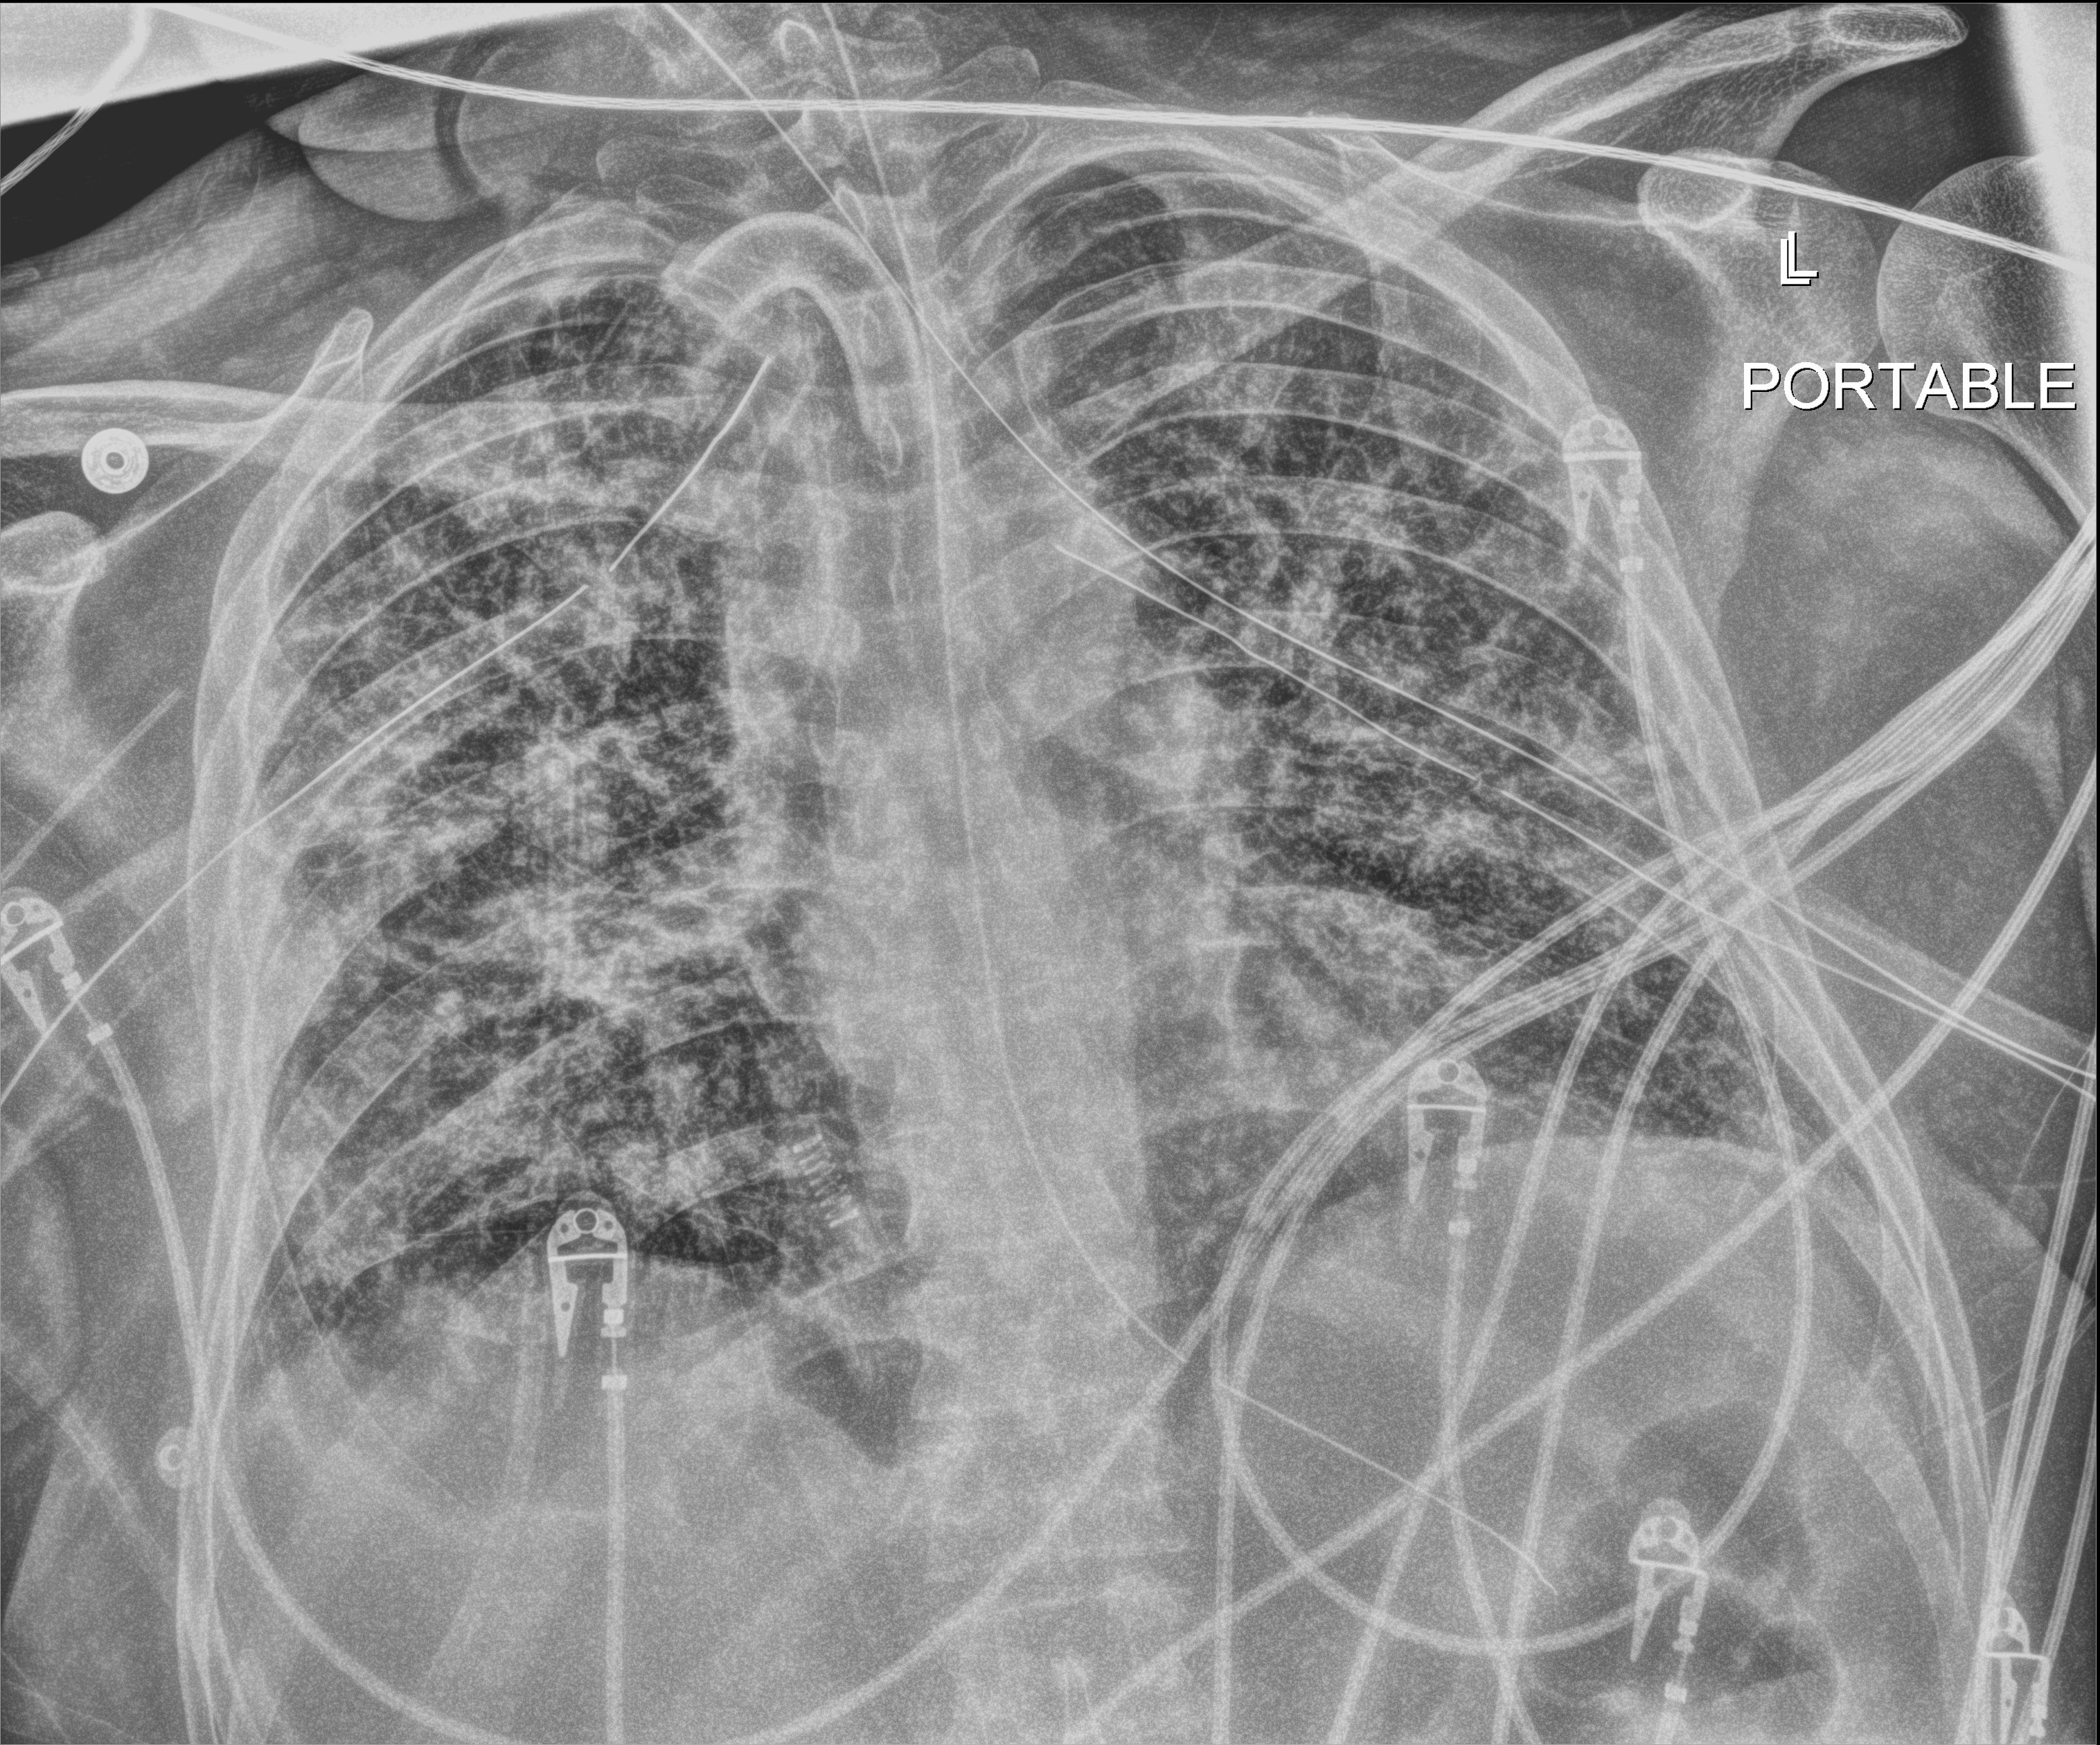
Chest radiograph (digital radiography); anteroposterior (AP) projection. Patient hospitalised with COVID-19; male, aged 18–59 years.
From the hospital-stay record, not from the radiograph (when in the stay this image was taken is not recorded): chronic kidney disease (admission record): no.